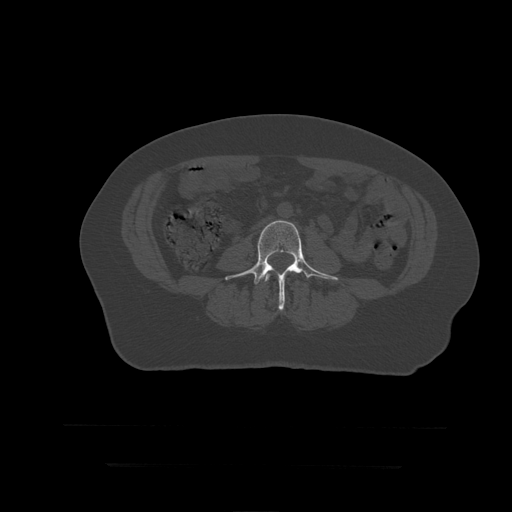
CT including the spine, one axial slice. Slice 102 of 399 in the series (ordered by position). Reconstruction kernel STANDARD. 120 kVp. Bone window (W 1800 / L 400 HU). 1.25 mm slice thickness. 512 × 512 image matrix, field of view 450 × 450 mm. Patient age 41 years. Case-level facts recorded for this patient, not image findings: primary cancer: breast.
Annotated regions visible in this slice (semi-automatic segmentation, software-assisted and operator-edited):
- L3 vertebra: bounding box (x1, y1, x2, y2) in pixels: (265, 273, 271, 282)
- L4 vertebra: (225, 221, 339, 311)